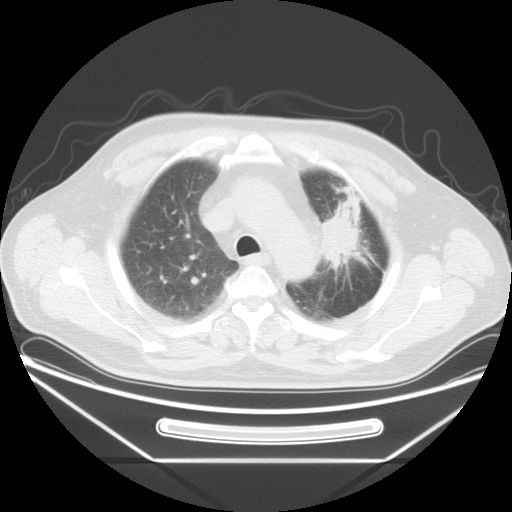
Chest CT, one axial slice; slice 30 of 38 in the series (ordered by position); 120 kVp; lung window (W 1500 / L -600 HU); 512 × 512 image matrix, field of view 411 × 411 mm. Male patient, age 61 years. Case-level facts recorded for this patient, not image findings: clinical TNM (as recorded): T2a N0 M0; histopathological grade: G3.
Structures marked on this image (rectangle marked by the reading radiologist):
- lung tumour (recorded histology: small cell carcinoma): box from (x=322, y=180) to (x=368, y=268) px